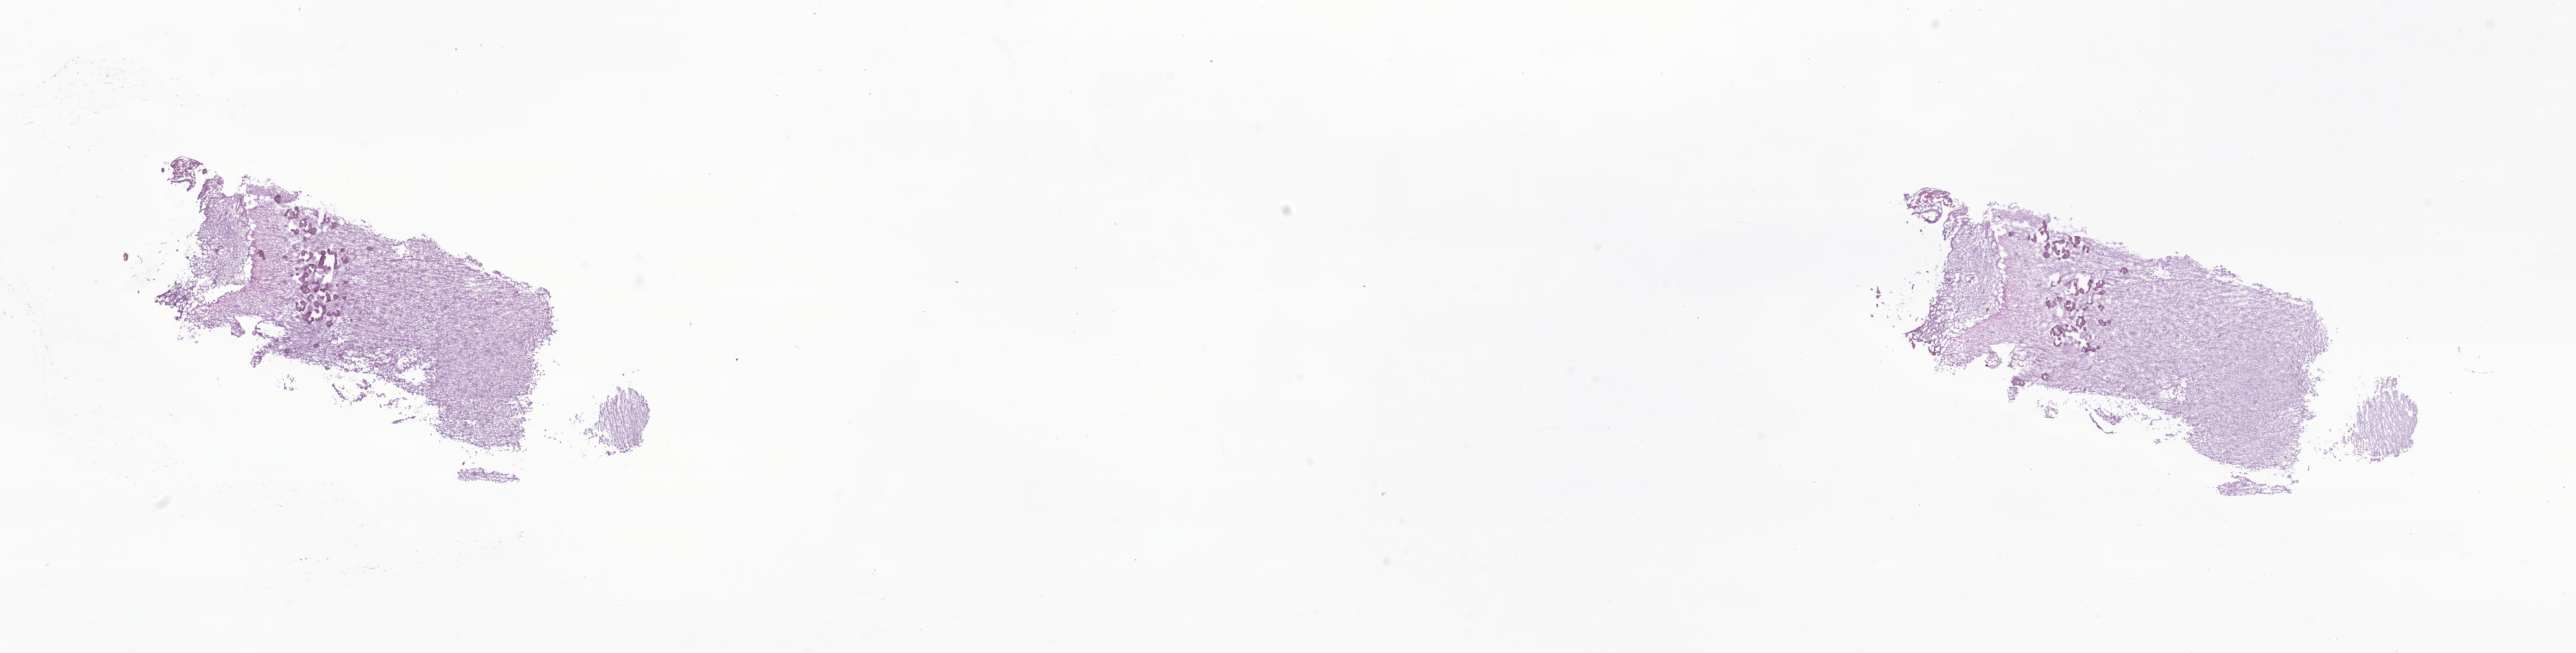
Haematoxylin and eosin whole-slide image of tumor tissue from the brain, whole scanned area (about 30.3 x 7.7 mm) shown as a low-resolution overview; cryosection (OCT / tissue freezing medium). Patient: female, age 224 months.
- diagnosis: Ganglioglioma, NOS